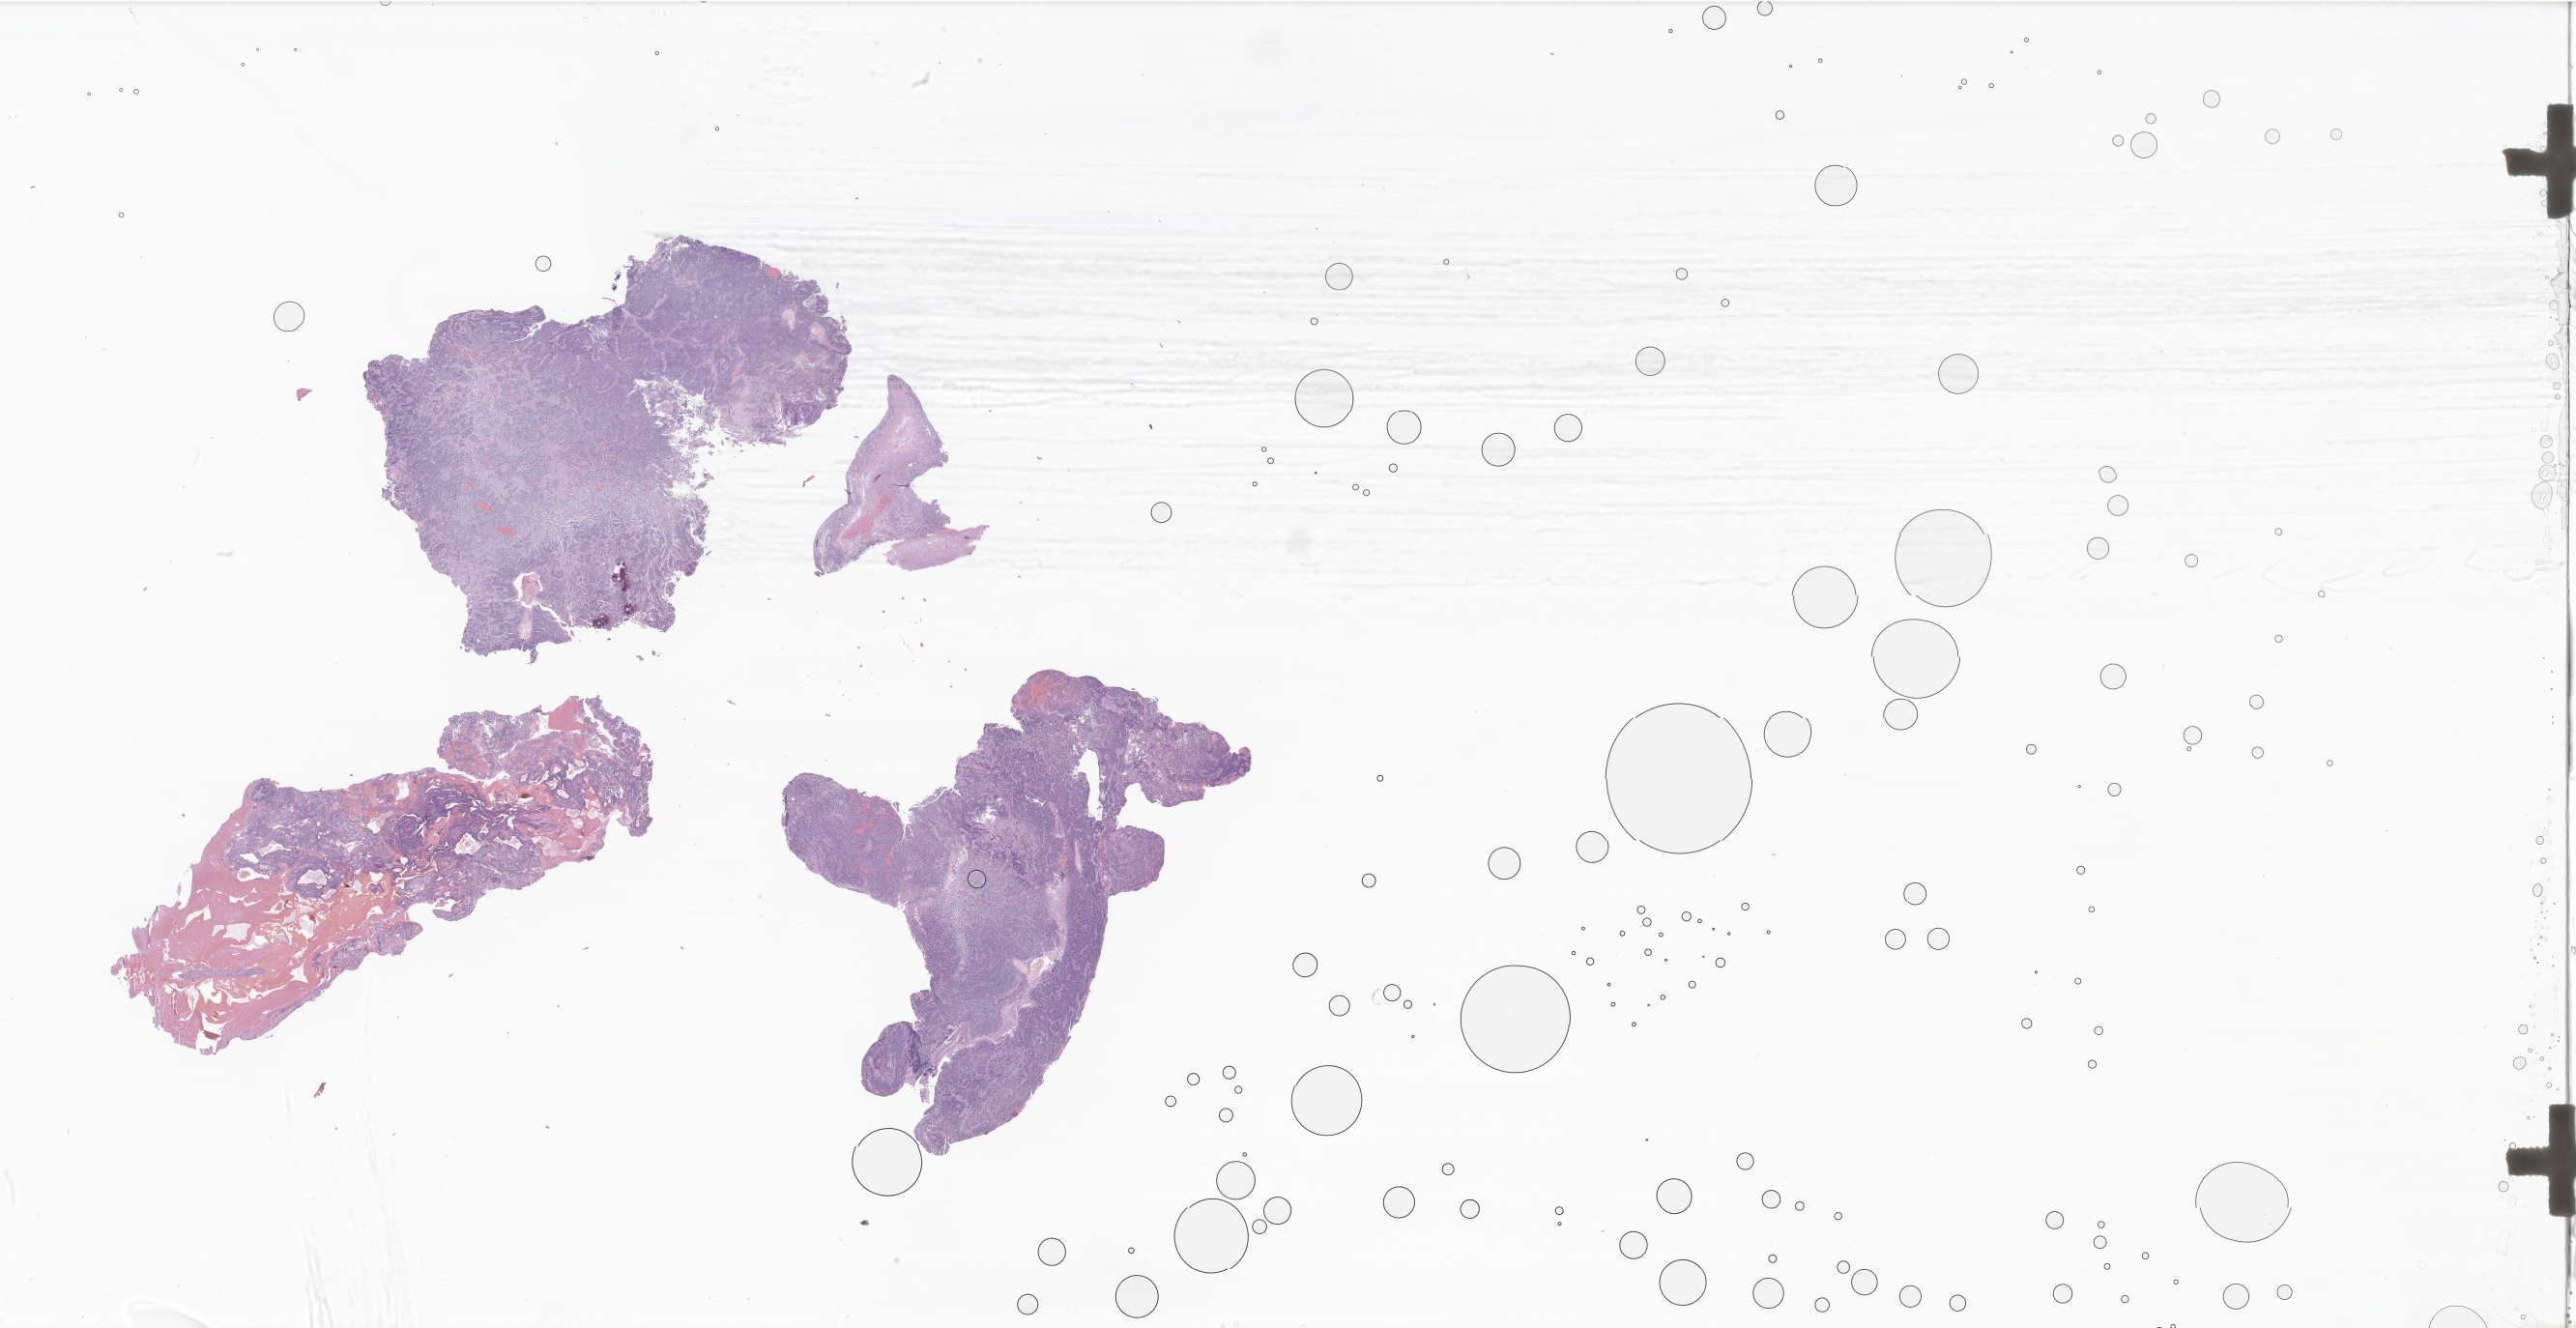
Hematoxylin and eosin (H&E) whole-slide image of tumor tissue from the pineal gland — shown as a low-resolution overview of the whole scanned area (about 45.0 x 23.2 mm). Formalin-fixed paraffin-embedded section. Female patient, age 155 months.
Diagnosis: Pineoblastoma.